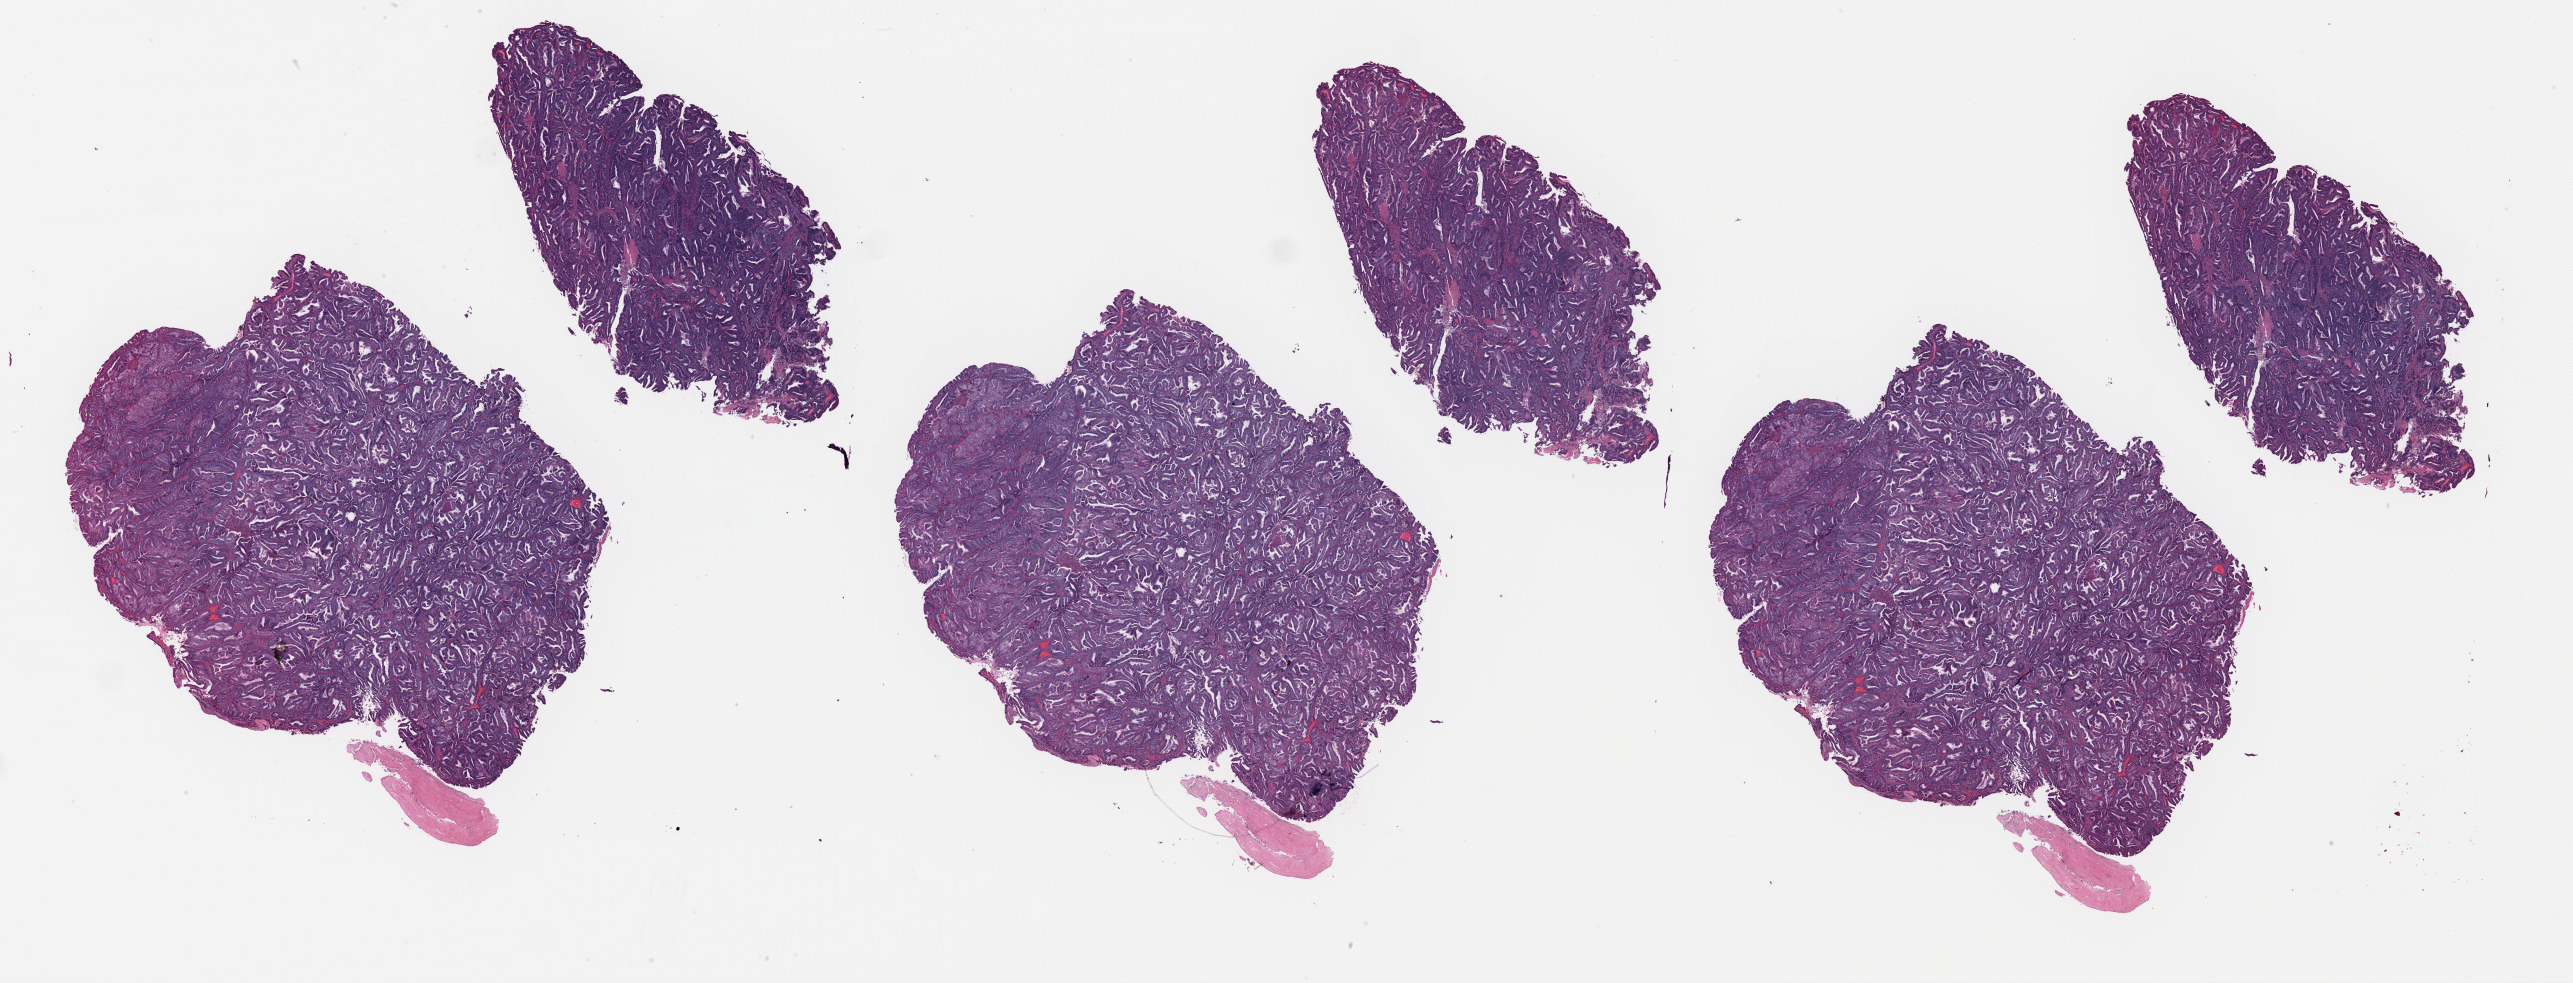
Digitized H&E tissue section (whole slide), low-resolution overview of the scanned area, about 40.6 x 15.5 mm. FFPE section. Uterus, primary tumour sample. Female patient; age at initial diagnosis 52 years. Histologic grade: G2 (moderately differentiated).
* pathologic diagnosis: Endometrioid adenocarcinoma, NOS (endometrium)
* lymph nodes positive (case pathology): 0 of 23 examined
* FIGO stage: IB